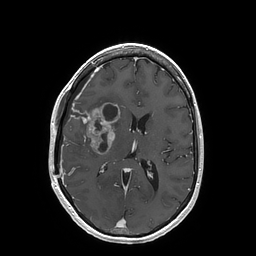
Brain MRI from a brain-tumour surgery series, one axial slice. Slice 77 of 202 in the series (ordered by position). T1-weighted post-contrast. 1 mm slice thickness. 256 × 256 image matrix, field of view 250 × 250 mm. Case-level facts recorded for this patient, not image findings: histopathology: Glioblastoma; WHO grade: 4.
Structures marked on this image (expert manual segmentation):
- tumour: bounding box (x1, y1, x2, y2) in pixels: (69, 103, 120, 154)